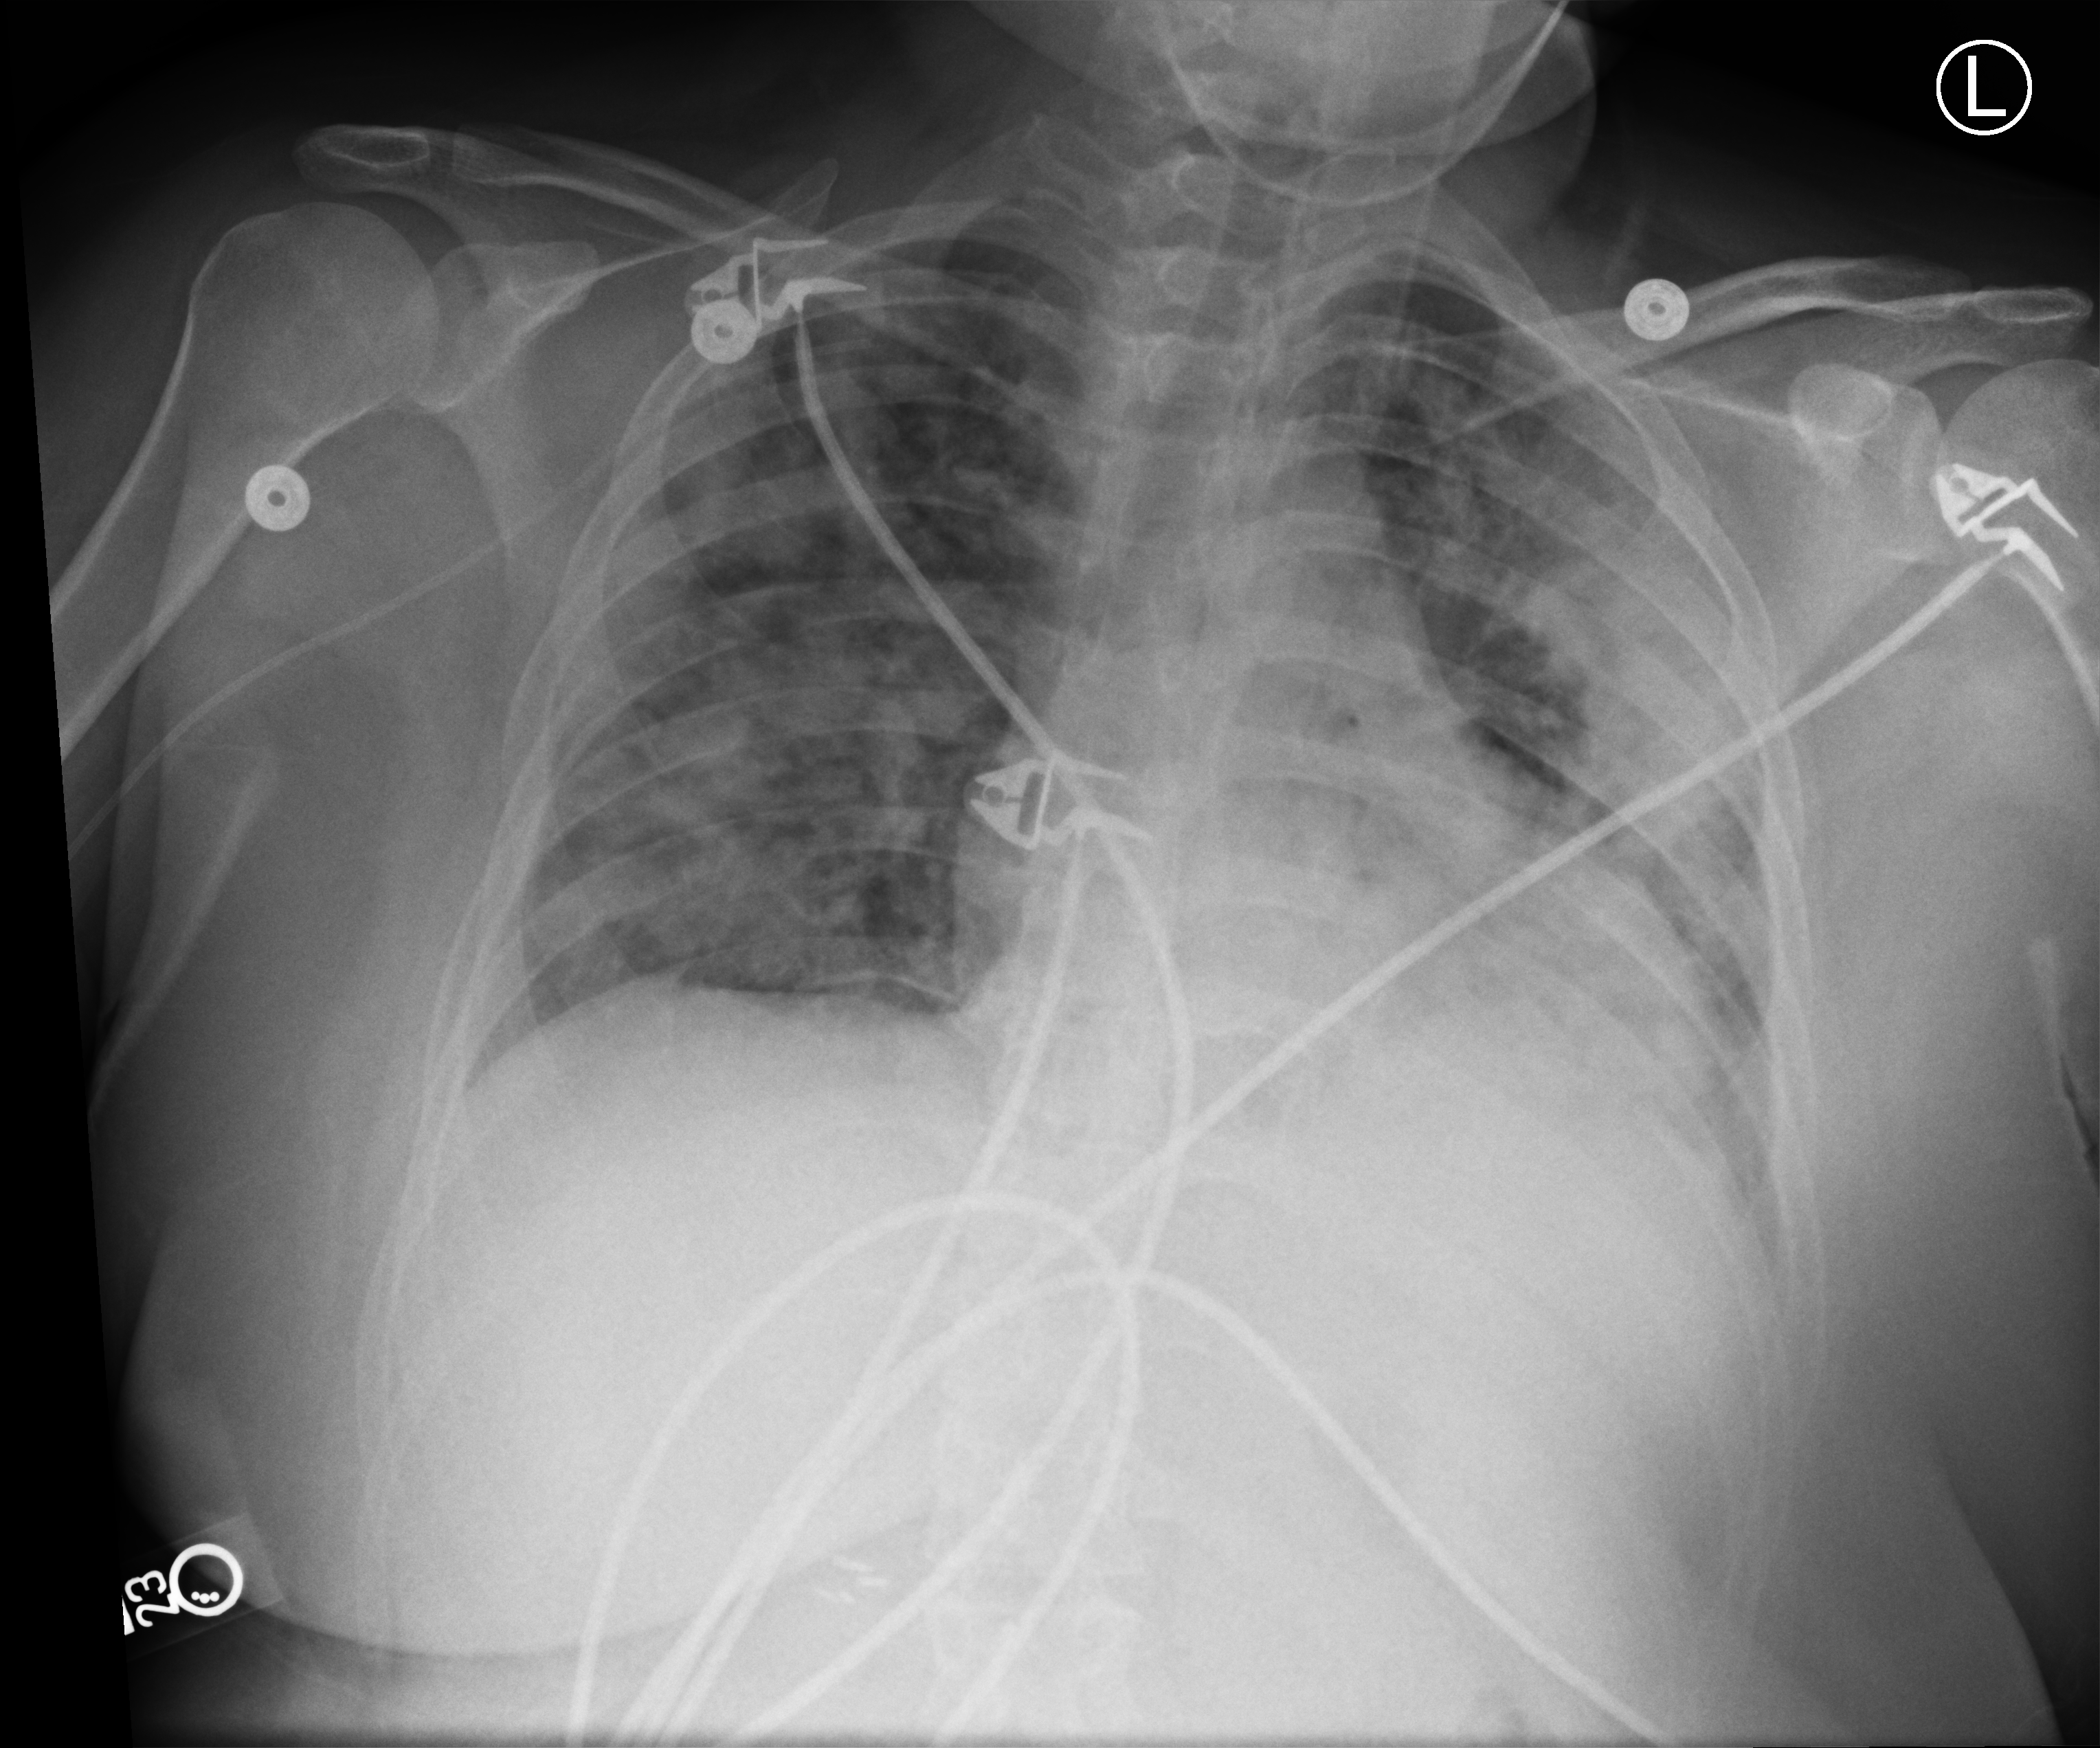
Bedside chest radiograph (computed radiography), anteroposterior (AP) projection. Patient hospitalised with COVID-19; female, aged 18–59 years.
From the hospital-stay record, not from the radiograph (when in the stay this image was taken is not recorded):
- admitted to intensive care during this hospital stay: no
- mechanically ventilated during this hospital stay: no